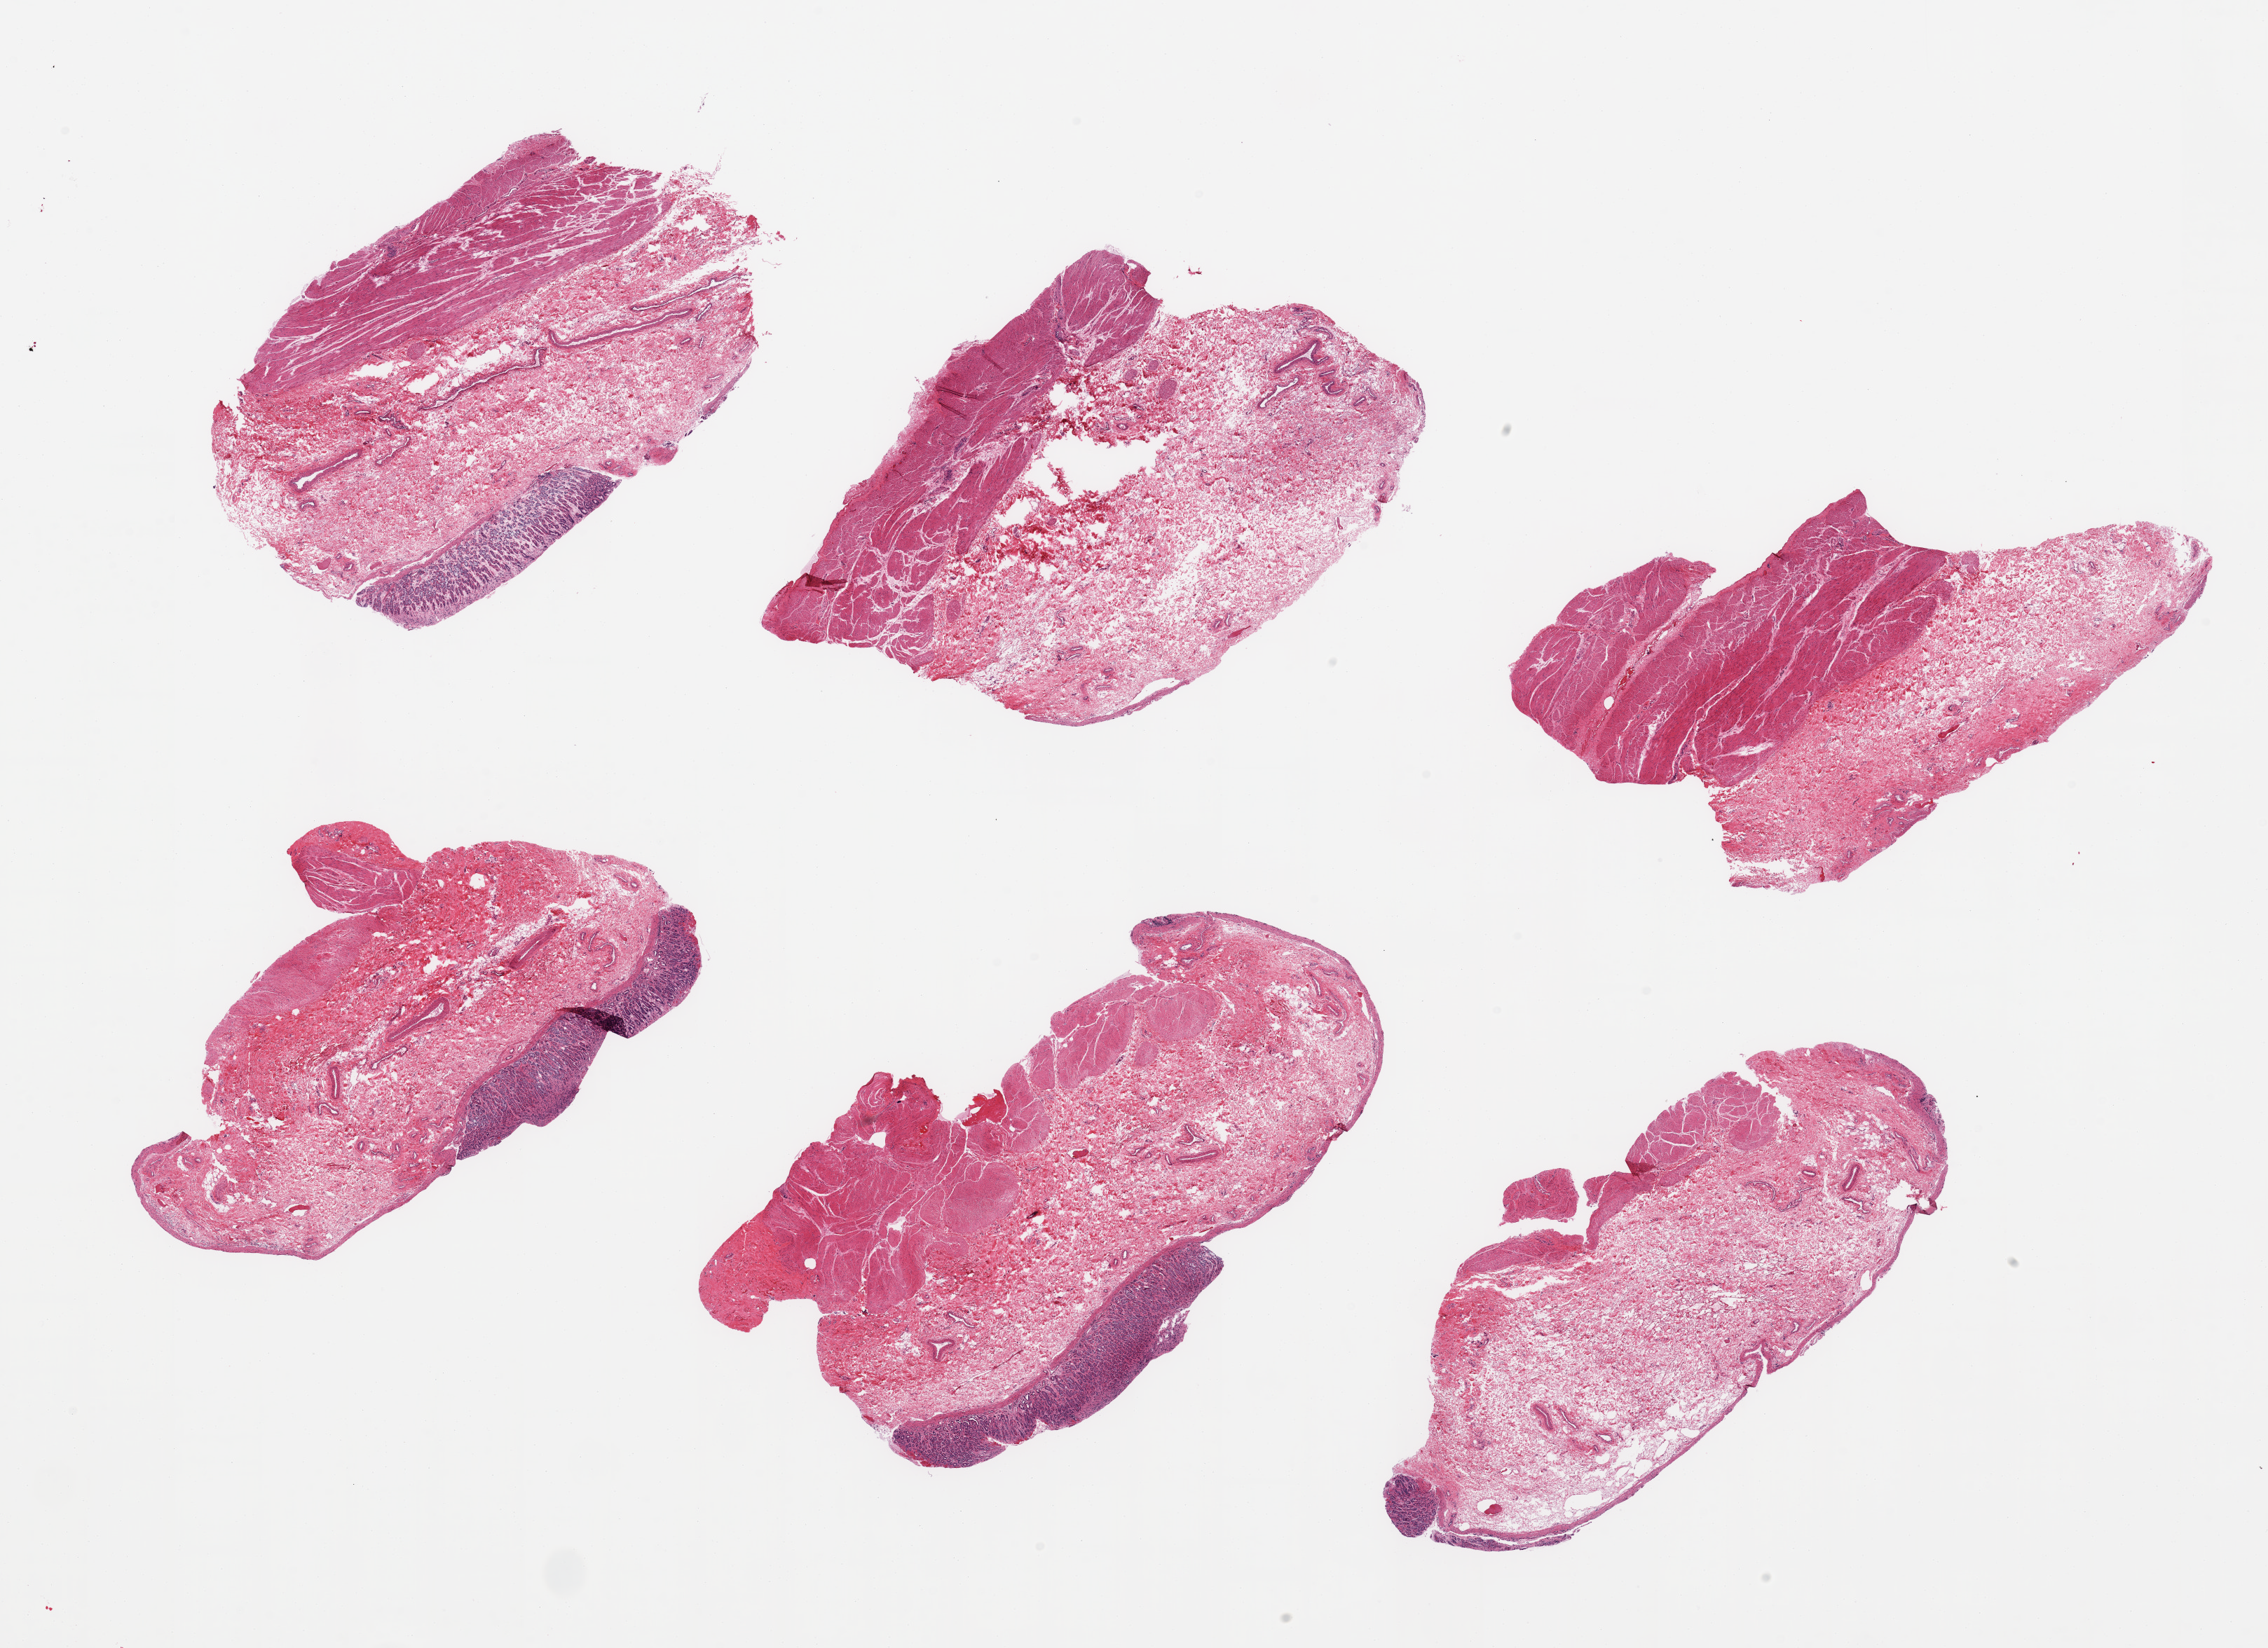
H&E whole-slide image, a low-resolution overview of the entire scanned area, about 25.6 x 18.6 mm. PAXgene-fixed, paraffin-embedded tissue. Target tissue: stomach. Tissue donor sample. Male donor.
Reviewer comment on this tissue sample: 6 pieces, mucosa up to ~0.8mm, partly denuded but well preserved, ~20% thickness.